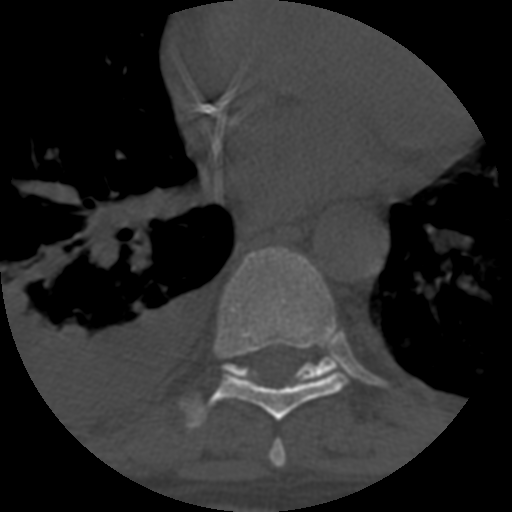
CT including the spine, one axial slice. Position 393 of 708 along the scan axis. Reconstruction kernel STANDARD. 120 kVp. One of 3 acquisitions stored at this slice position. Bone window (W 1800 / L 400 HU). 1.25 mm slice thickness. 512 × 512 image matrix, field of view 160 × 160 mm. Patient age 55 years. From the clinical record (not read from this slice): primary cancer: colon.
Structures marked on this image (semi-automatically segmented with operator editing):
- T7 vertebra: bounding box [x1, y1, x2, y2] px = [270, 441, 286, 467]
- T8 vertebra: [189, 247, 348, 427]
- T9 vertebra: [223, 356, 339, 383]